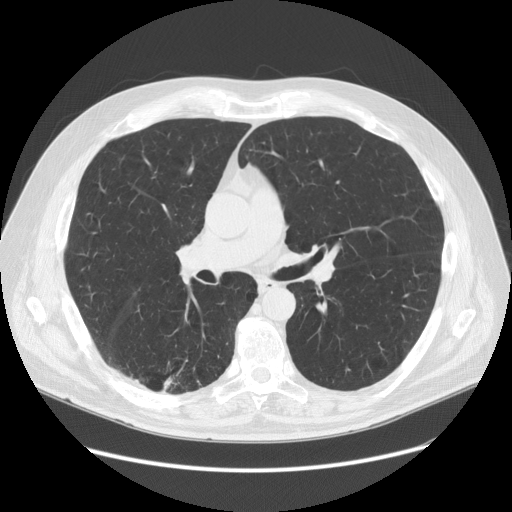
Low-dose screening chest CT, one axial slice. Position 82 of 149 along the scan axis. 120 kVp. Lung window (W 1500 / L -600 HU). 512 × 512 image matrix, field of view 400 × 400 mm.
Annotated regions visible in this slice (outlined manually by an expert reader):
- lesion 1 (tumor, lower lobe of right lung): box from (x=162, y=375) to (x=172, y=393) px